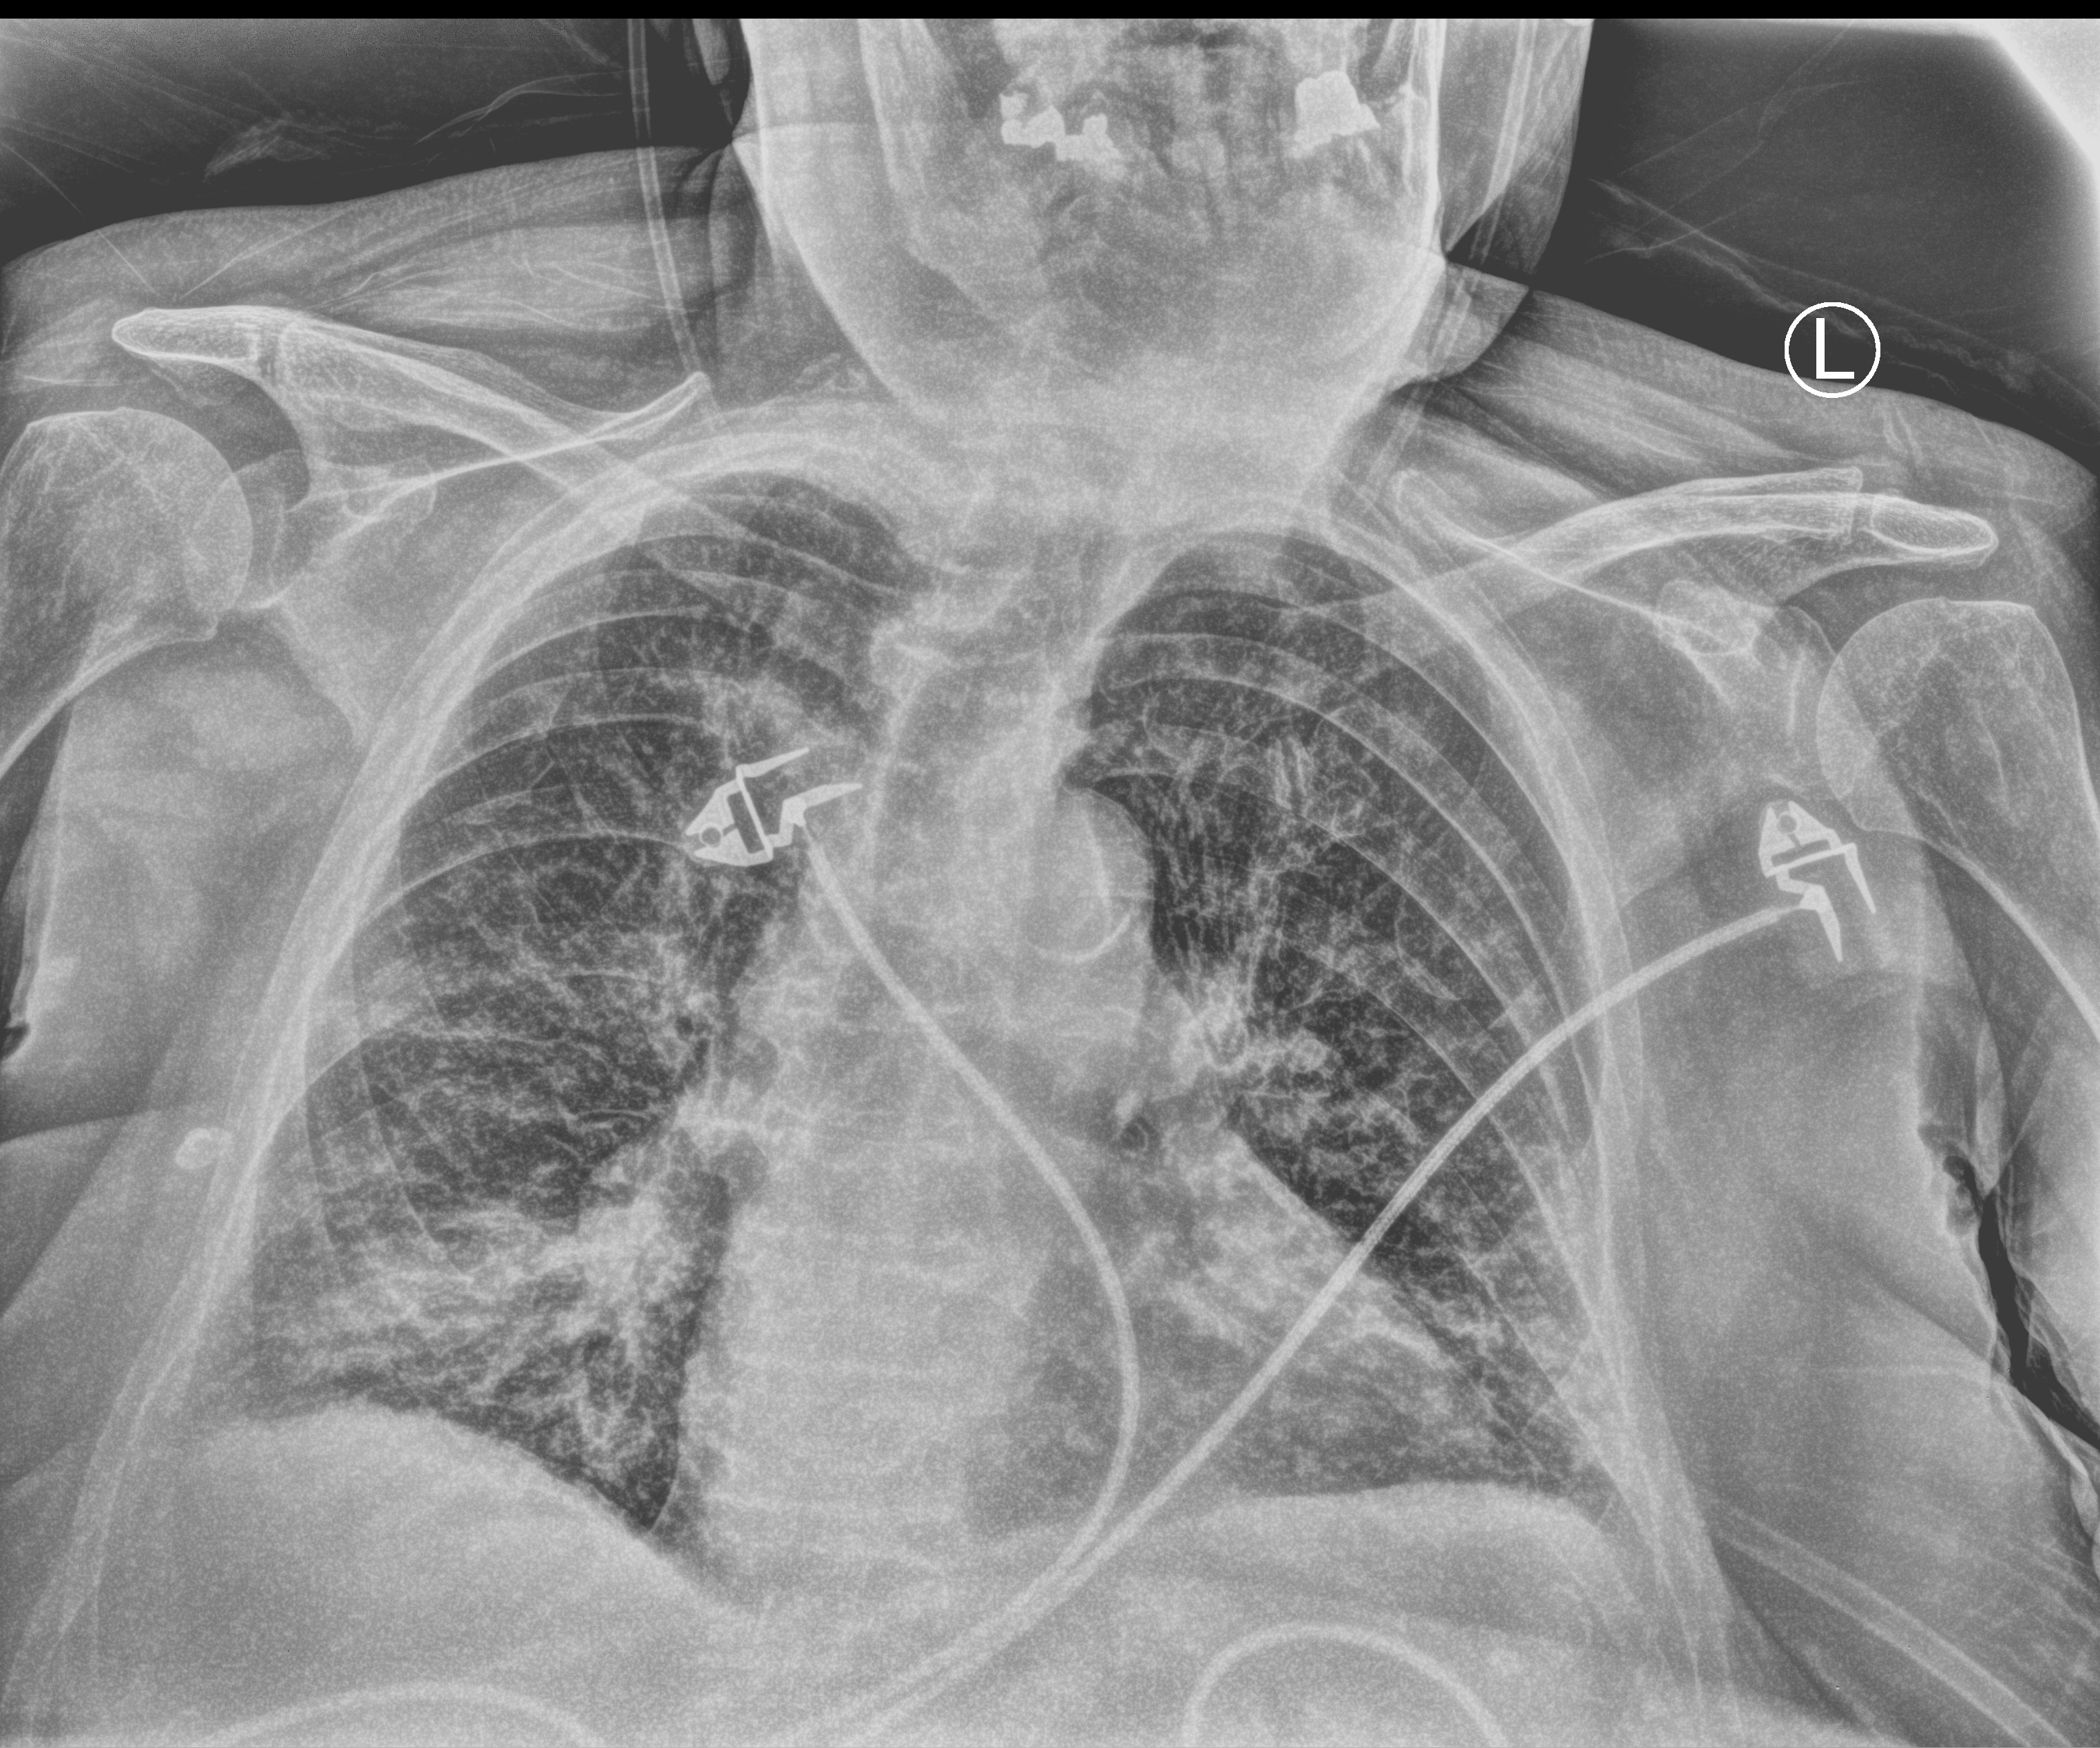
Chest X-ray (portable); anteroposterior (AP) projection. Female patient hospitalised with COVID-19, age 75–90 years.
Admission-level facts for this patient (not findings on this image; timing relative to this image not recorded):
- chronic kidney disease (admission record): yes
- mechanically ventilated during this hospital stay: no
- admitted to intensive care during this hospital stay: no